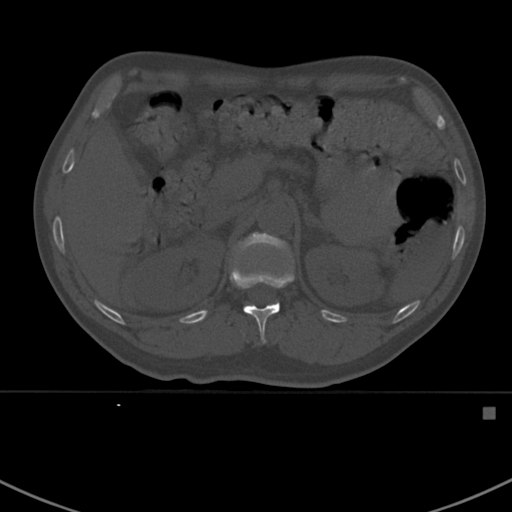
CT including the spine, one axial slice; position 324 of 412 along the scan axis; reconstruction kernel Br40s; 120 kVp; bone window (W 1800 / L 400 HU); 1.5 mm slice thickness; 512 × 512 image matrix, field of view 358 × 358 mm. Male patient, age 59 years. Case-level facts recorded for this patient, not image findings: primary cancer: prostate.
Annotated regions visible in this slice (semi-automatically segmented with operator editing):
- L1 vertebra: bounding box [x1, y1, x2, y2] px = [234, 233, 291, 256]
- T12 vertebra: [230, 266, 294, 344]